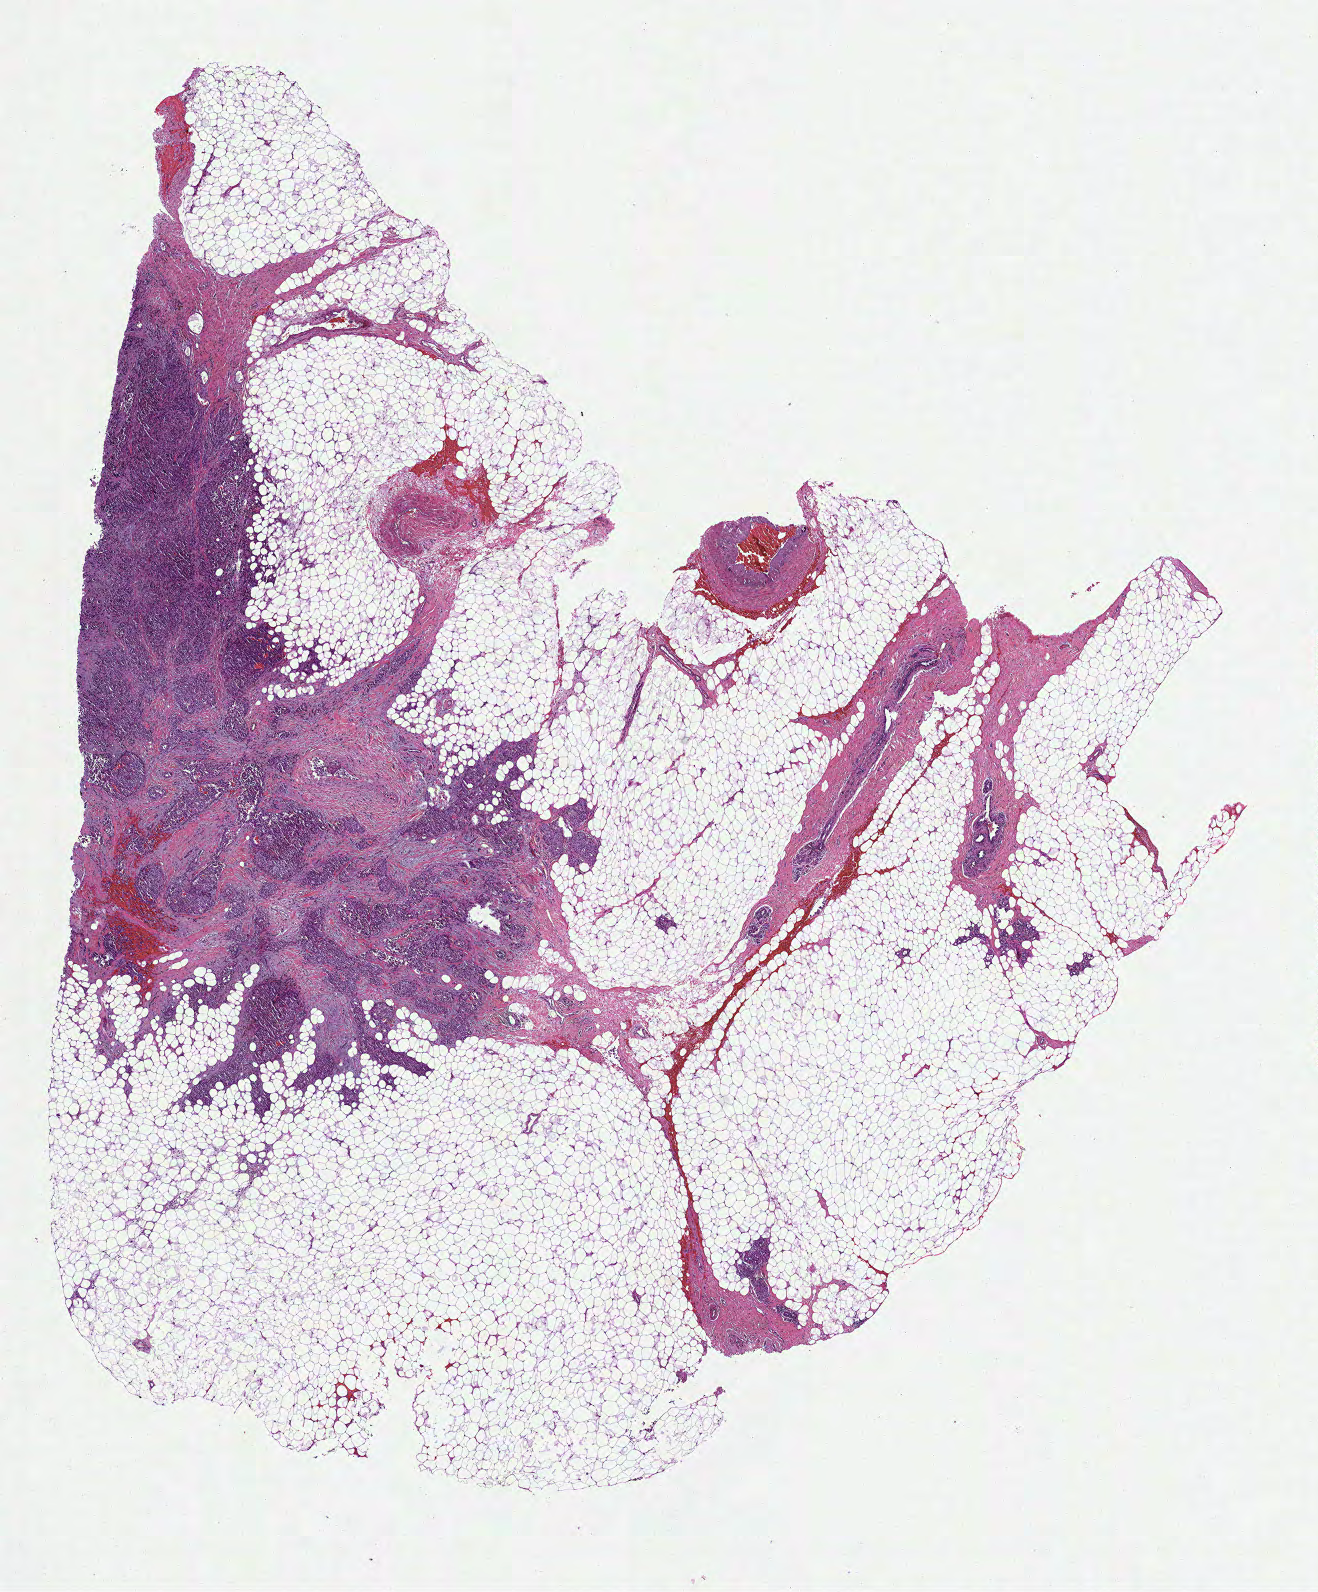
Digitized H&E-stained tissue section (whole slide), whole scanned area (about 10.6 x 12.8 mm) shown as a low-resolution overview; formalin-fixed paraffin-embedded (FFPE) diagnostic section; breast, primary tumour sample. Female patient; age at initial diagnosis 51 years.
* diagnosis: Infiltrating duct carcinoma, NOS
* AJCC pathologic stage: IIA
* TNM: T1c N1a MX